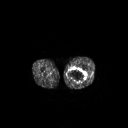
FDG PET of an extremity soft-tissue mass (from a PET/CT study), one axial slice. Slice 232 of 267 in the series (ordered by position). 3.27 mm slice thickness. 128 × 128 image matrix. Male patient, age 44 years. Case-level facts recorded for this patient, not image findings: histological type: undifferentiated pleomorphic liposarcoma; grade: high; site of the primary tumour: left thigh.
Structures marked on this image (expert contour drawn on MRI and transferred to this co-registered scan by the dataset authors):
- gross tumour volume including surrounding oedema: bounding box [x1, y1, x2, y2] px = [67, 67, 87, 83]
- gross tumour volume (mass): [67, 67, 87, 83]